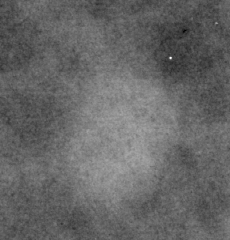
Region of interest cut from a scanned film mammogram (one marked finding); right breast; MLO view.
Mass, shape oval / lymph node, margins circumscribed; BI-RADS assessment category 2; benign without callback (not worked up further).